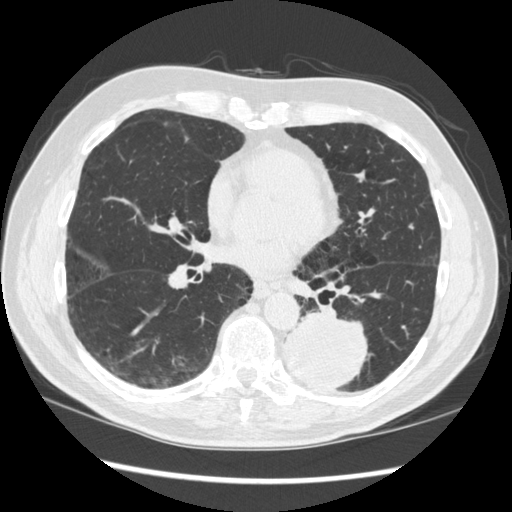
Low-dose screening chest CT, one axial slice. Position 148 of 348 along the scan axis. 120 kVp. Lung window (W 1500 / L -600 HU). 1.25 mm slice thickness. 512 × 512 image matrix.
Structures marked on this image (outlined manually by an expert reader):
- lesion 1 (tumor, lower lobe of left lung): bounding box (x1, y1, x2, y2) in pixels: (284, 312, 369, 390)